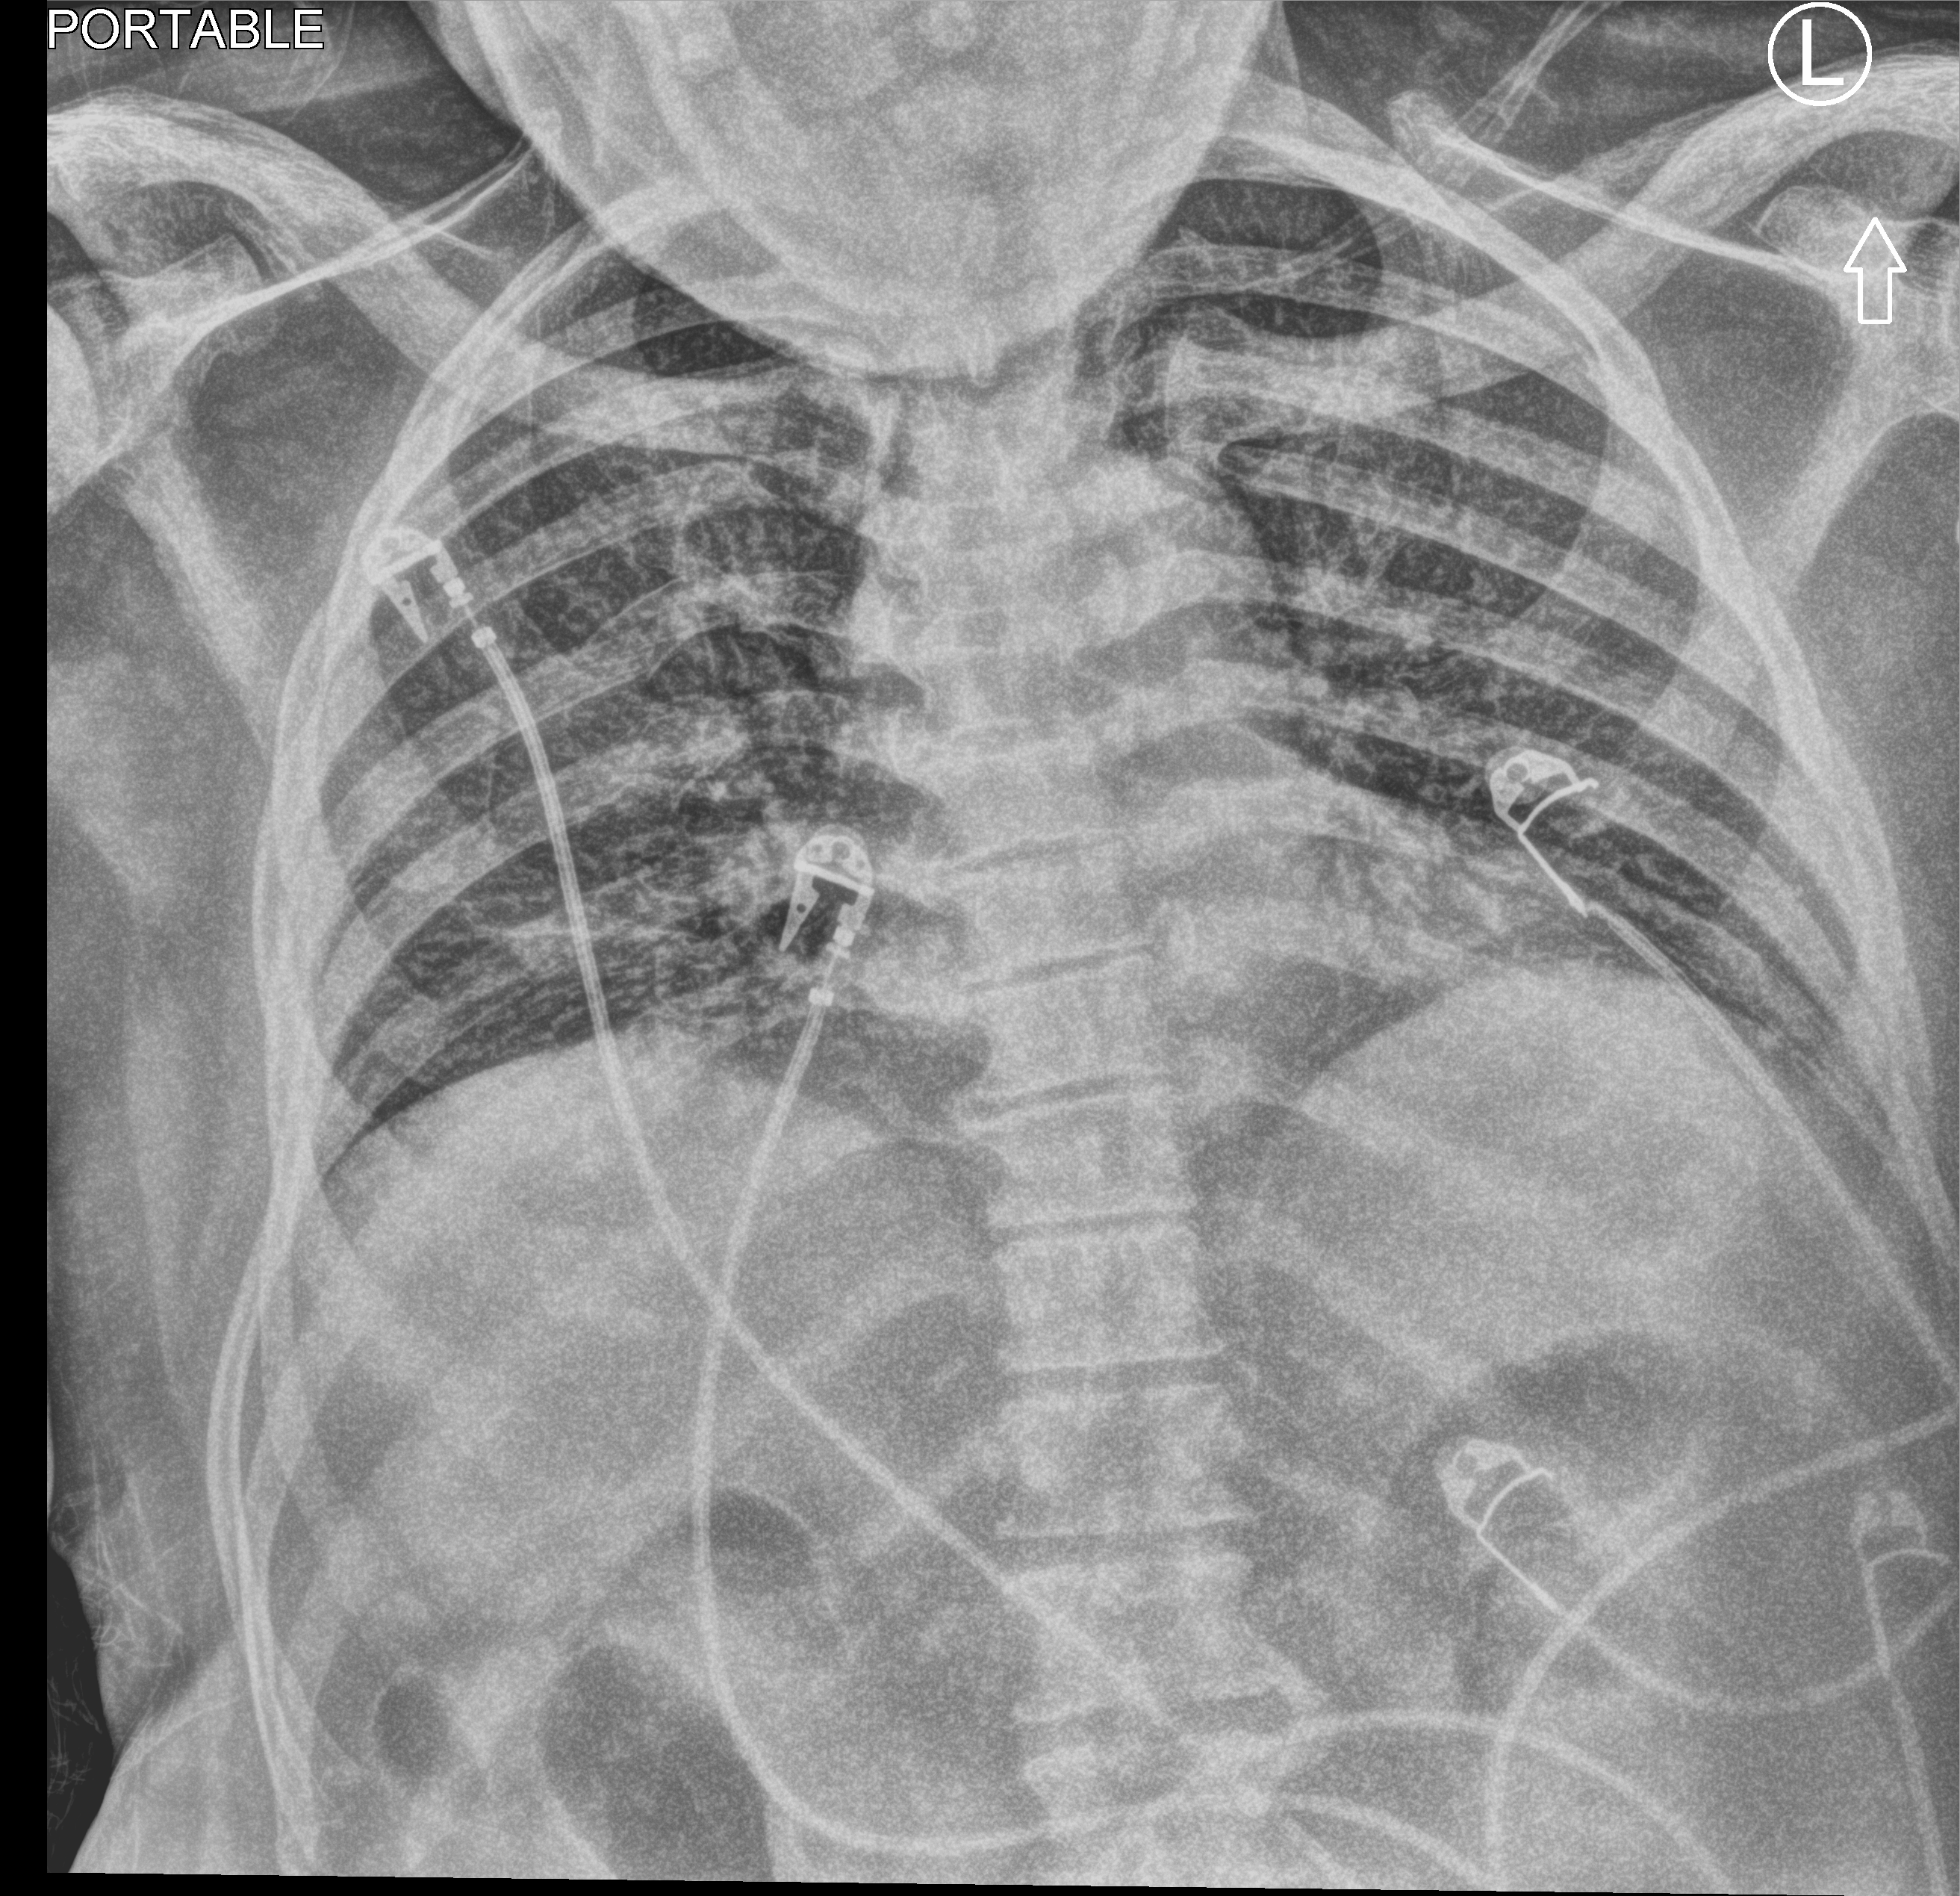
Portable chest radiograph, anteroposterior (AP) projection. Male patient hospitalised with COVID-19, age 60–74 years.
Admission-level facts for this patient (not findings on this image; timing relative to this image not recorded):
- diabetes (admission record): yes
- length of hospital stay: 8 days
- admitted to intensive care during this hospital stay: no